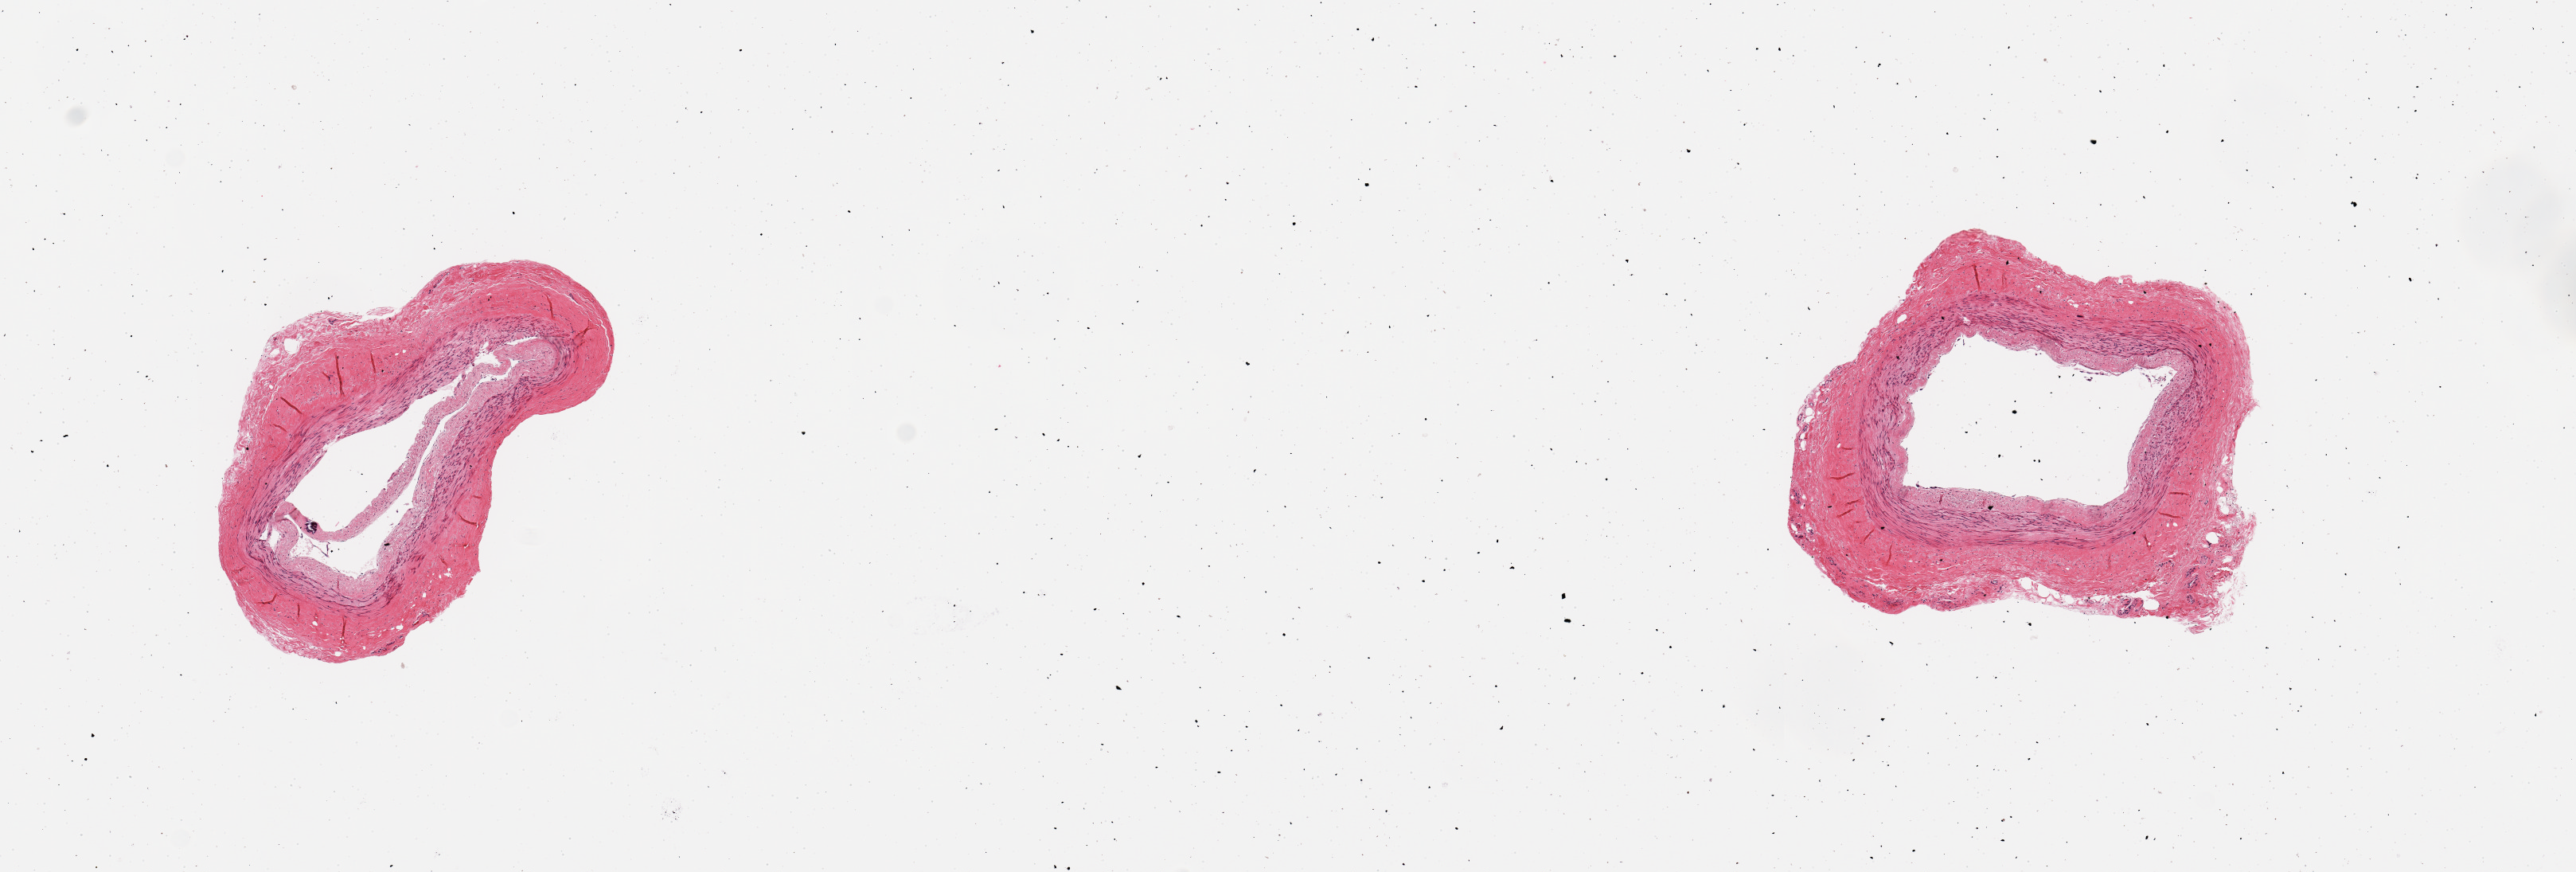
Hematoxylin and eosin (H&E) whole-slide image — a low-resolution overview of the entire scanned area, about 12.8 x 4.3 mm (slide scanned at 20x); PAXgene-fixed paraffin-embedded (PFPE) section; section of tibial artery (target tissue); donor tissue sample. Donor sex: female.
• review note (as recorded): 2 pieces; no plaques; microcalcification; well trimmed